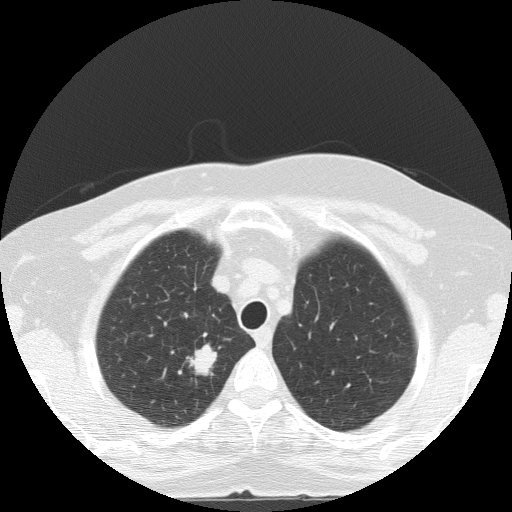
Axial slice from a low-dose chest CT screening exam, baseline screening round, lung window (W 1500 / L -600 HU), 2 mm slice thickness, lung (sharp) reconstruction kernel (FC51), 120 kVp, slice 23 of 133 in the series. Female, age 56 years at enrolment. Current smoker at enrolment.
Lesion marked by an expert reader, bounding box [x1, y1, x2, y2] px = [171, 338, 235, 389]. The screening reader recorded 2 non-calcified nodules or masses ≥4 mm on this exam (right upper lobe, right lower lobe); which of them this box marks is not recorded. Official screen result: positive, change unspecified: nodule(s) >= 4 mm or enlarging nodule(s), mass(es), or other non-specific abnormalities suspicious for lung cancer. Lung cancer was diagnosed 24 days after this screen: adenocarcinoma, NOS, right upper lobe, poorly differentiated (G3), stage IA (AJCC 6th edition), 20 mm at pathology.